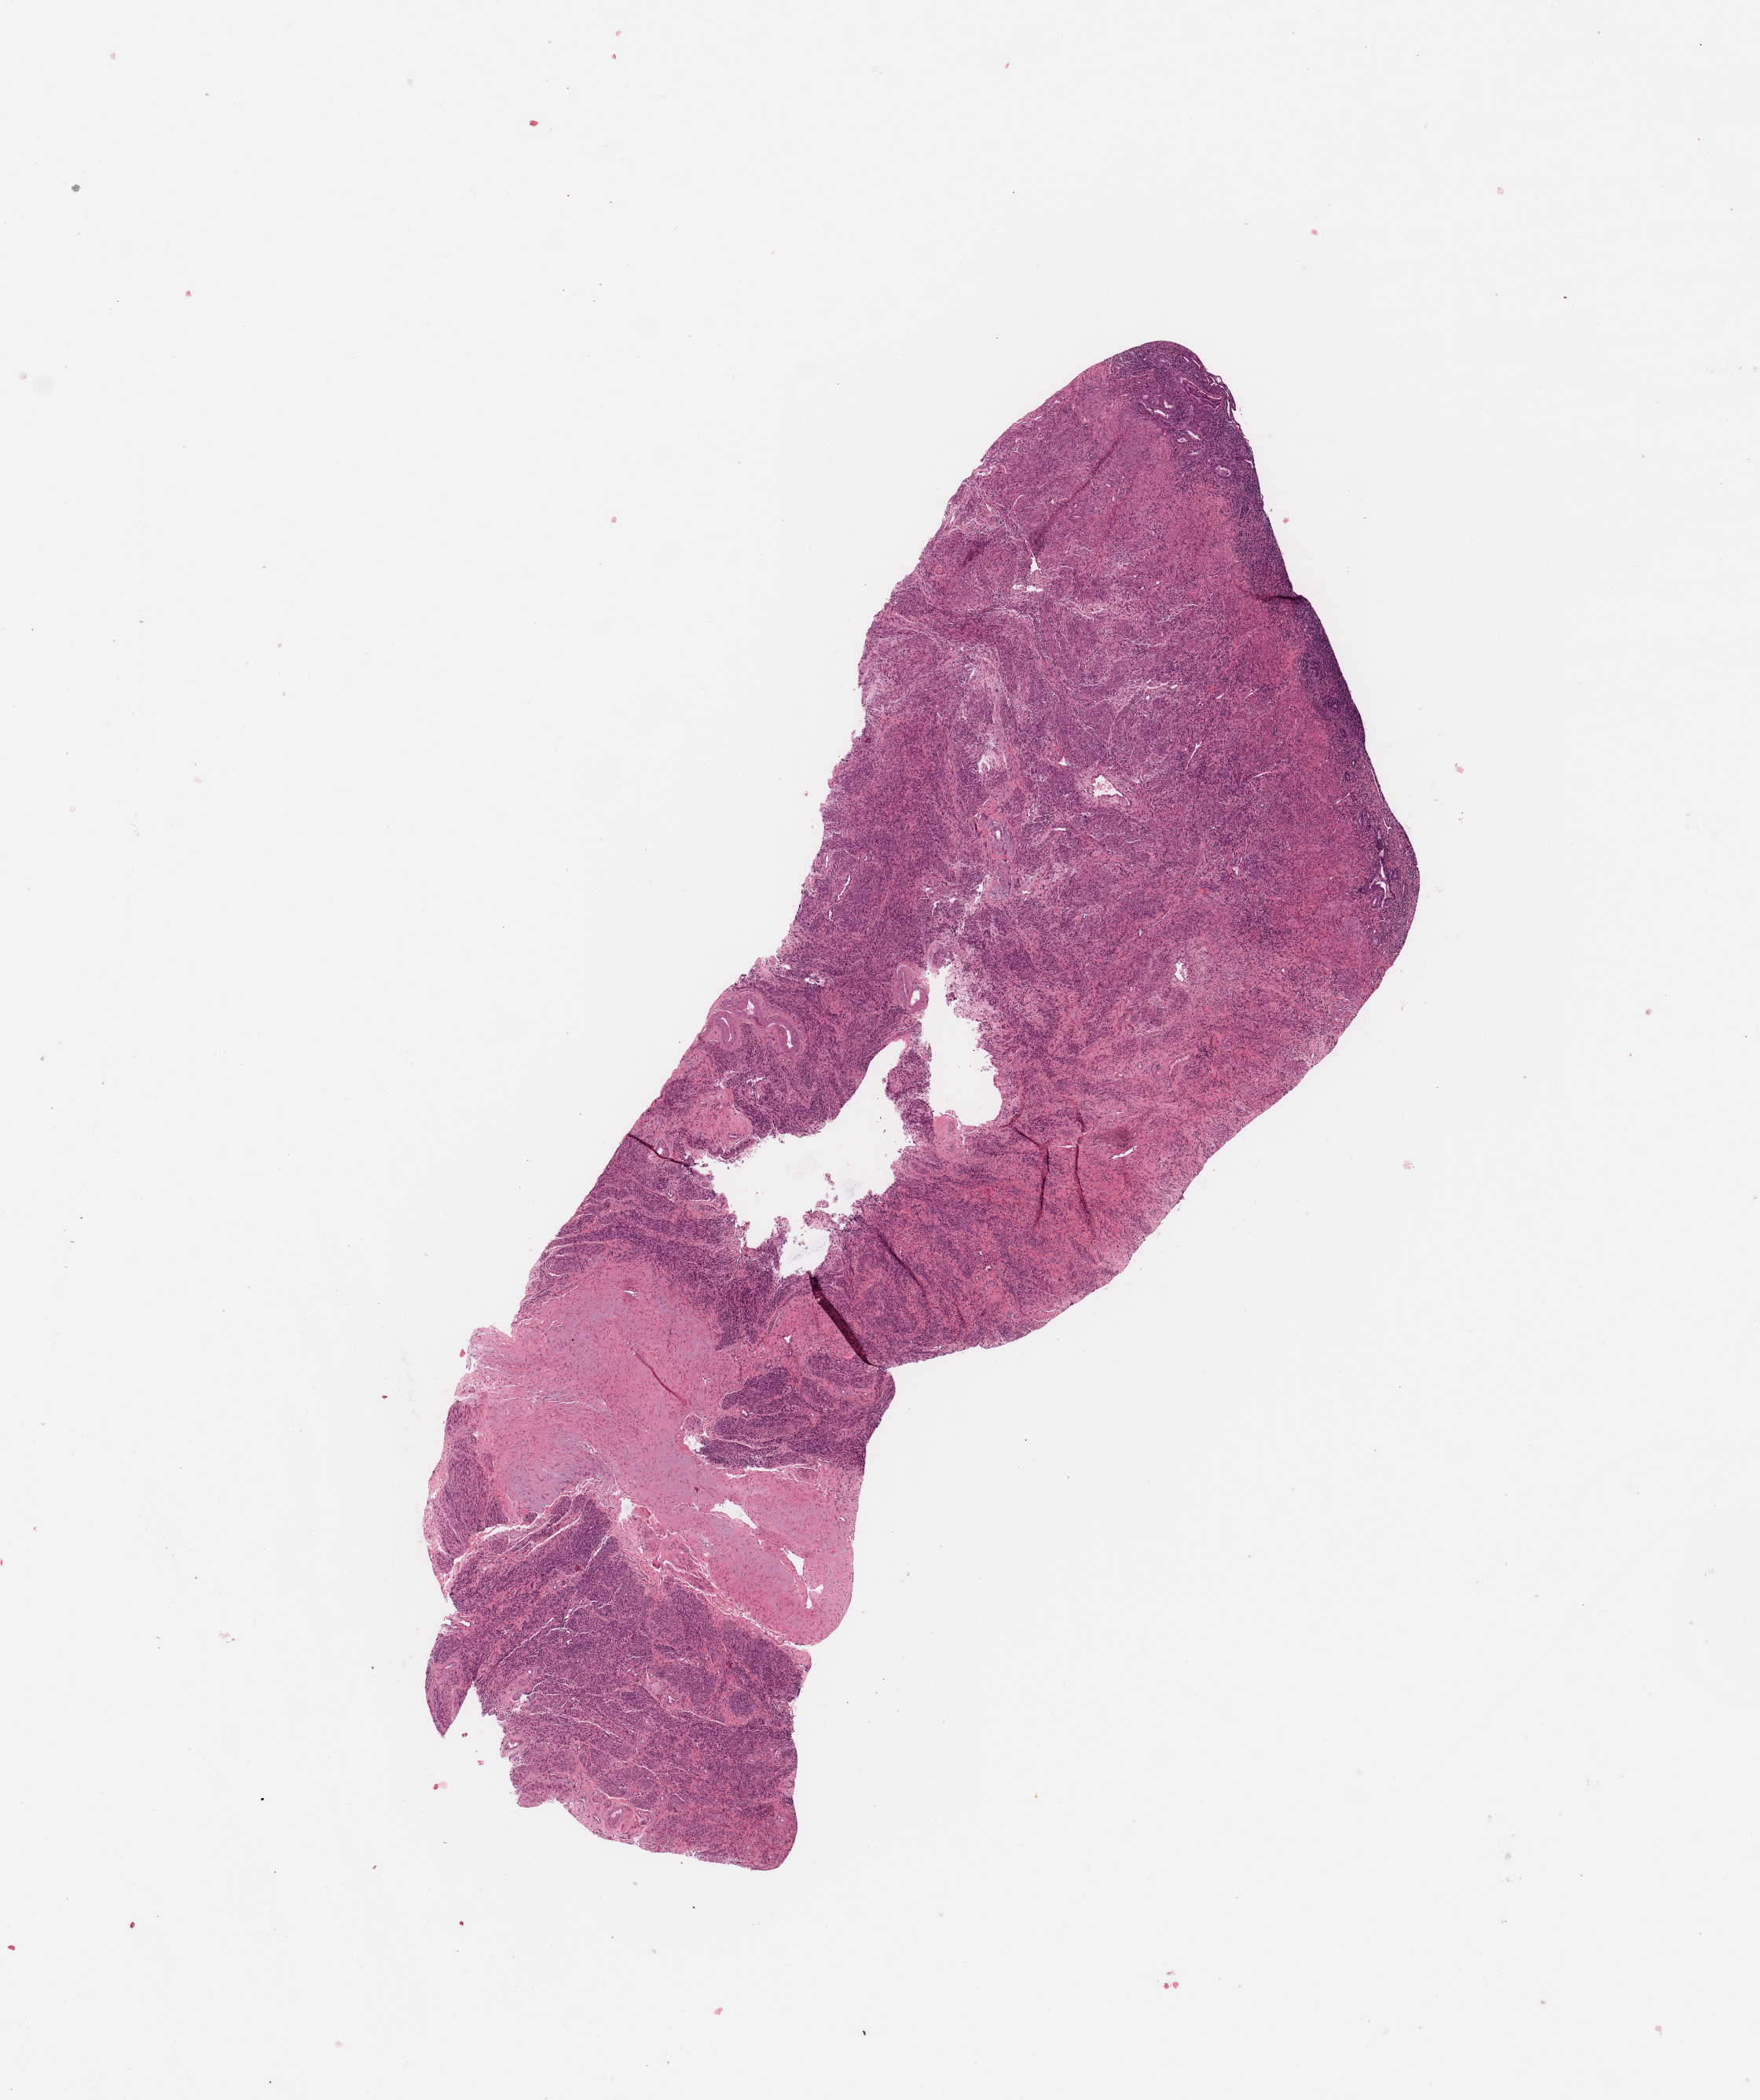
Whole-slide histology image, H&E, low-resolution overview of the scanned area, about 8.9 x 10.6 mm (acquisition: 20x scan), normal (non-tumour) tissue sample, uterus. Female, 73 y/o.
- this section: normal (non-tumour) tissue from the same patient
- patient diagnosis: Endometrioid adenocarcinoma, NOS